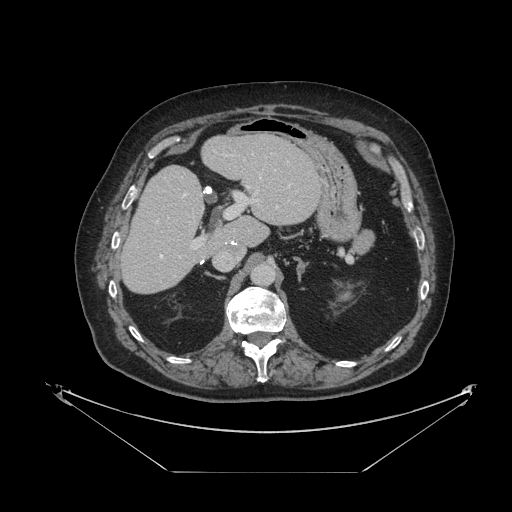
Contrast-enhanced abdominal CT, one axial slice; position 62 of 121 along the scan axis; reconstruction kernel STANDARD; 120 kVp; intravenous contrast given; soft-tissue window (W 400 / L 40 HU); 2.5 mm slice thickness; 512 × 512 image matrix. Male patient, age 68 years. From the clinical record (not read from this slice): diagnosis: colorectal cancer liver metastases, imaged before liver resection; multiple liver metastases: no; largest metastasis: 4 cm.
Structures marked on this image (expert manual segmentation):
- hepatic veins: bounding box [x1, y1, x2, y2] px = [160, 185, 290, 258]
- liver: [122, 136, 321, 294]
- planned liver remnant (the part of the liver to remain after resection): [122, 136, 321, 294]
- portal vein (with intrahepatic branches): [191, 177, 261, 249]